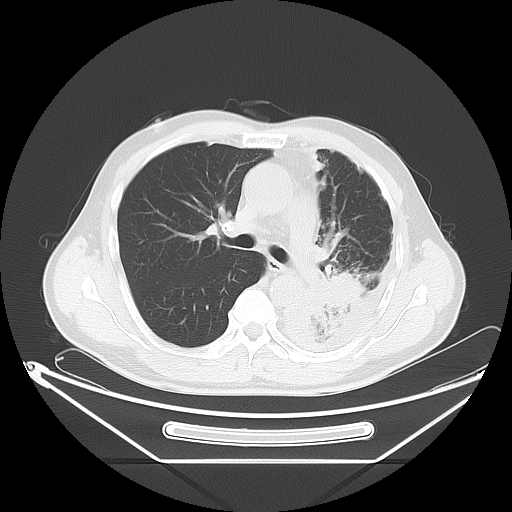
Chest CT, one axial slice; slice 39 of 63 in the series (ordered by position); lung window (W 1500 / L -600 HU); 512 × 512 image matrix, field of view 442 × 442 mm. Male patient, age 60 years. From the clinical record (not read from this slice): clinical TNM (as recorded): T4 N1 M1.
Annotated regions visible in this slice (bounding box drawn by a radiologist):
- lung tumour (recorded histology: adenocarcinoma): bounding box [x1, y1, x2, y2] px = [299, 266, 375, 324]